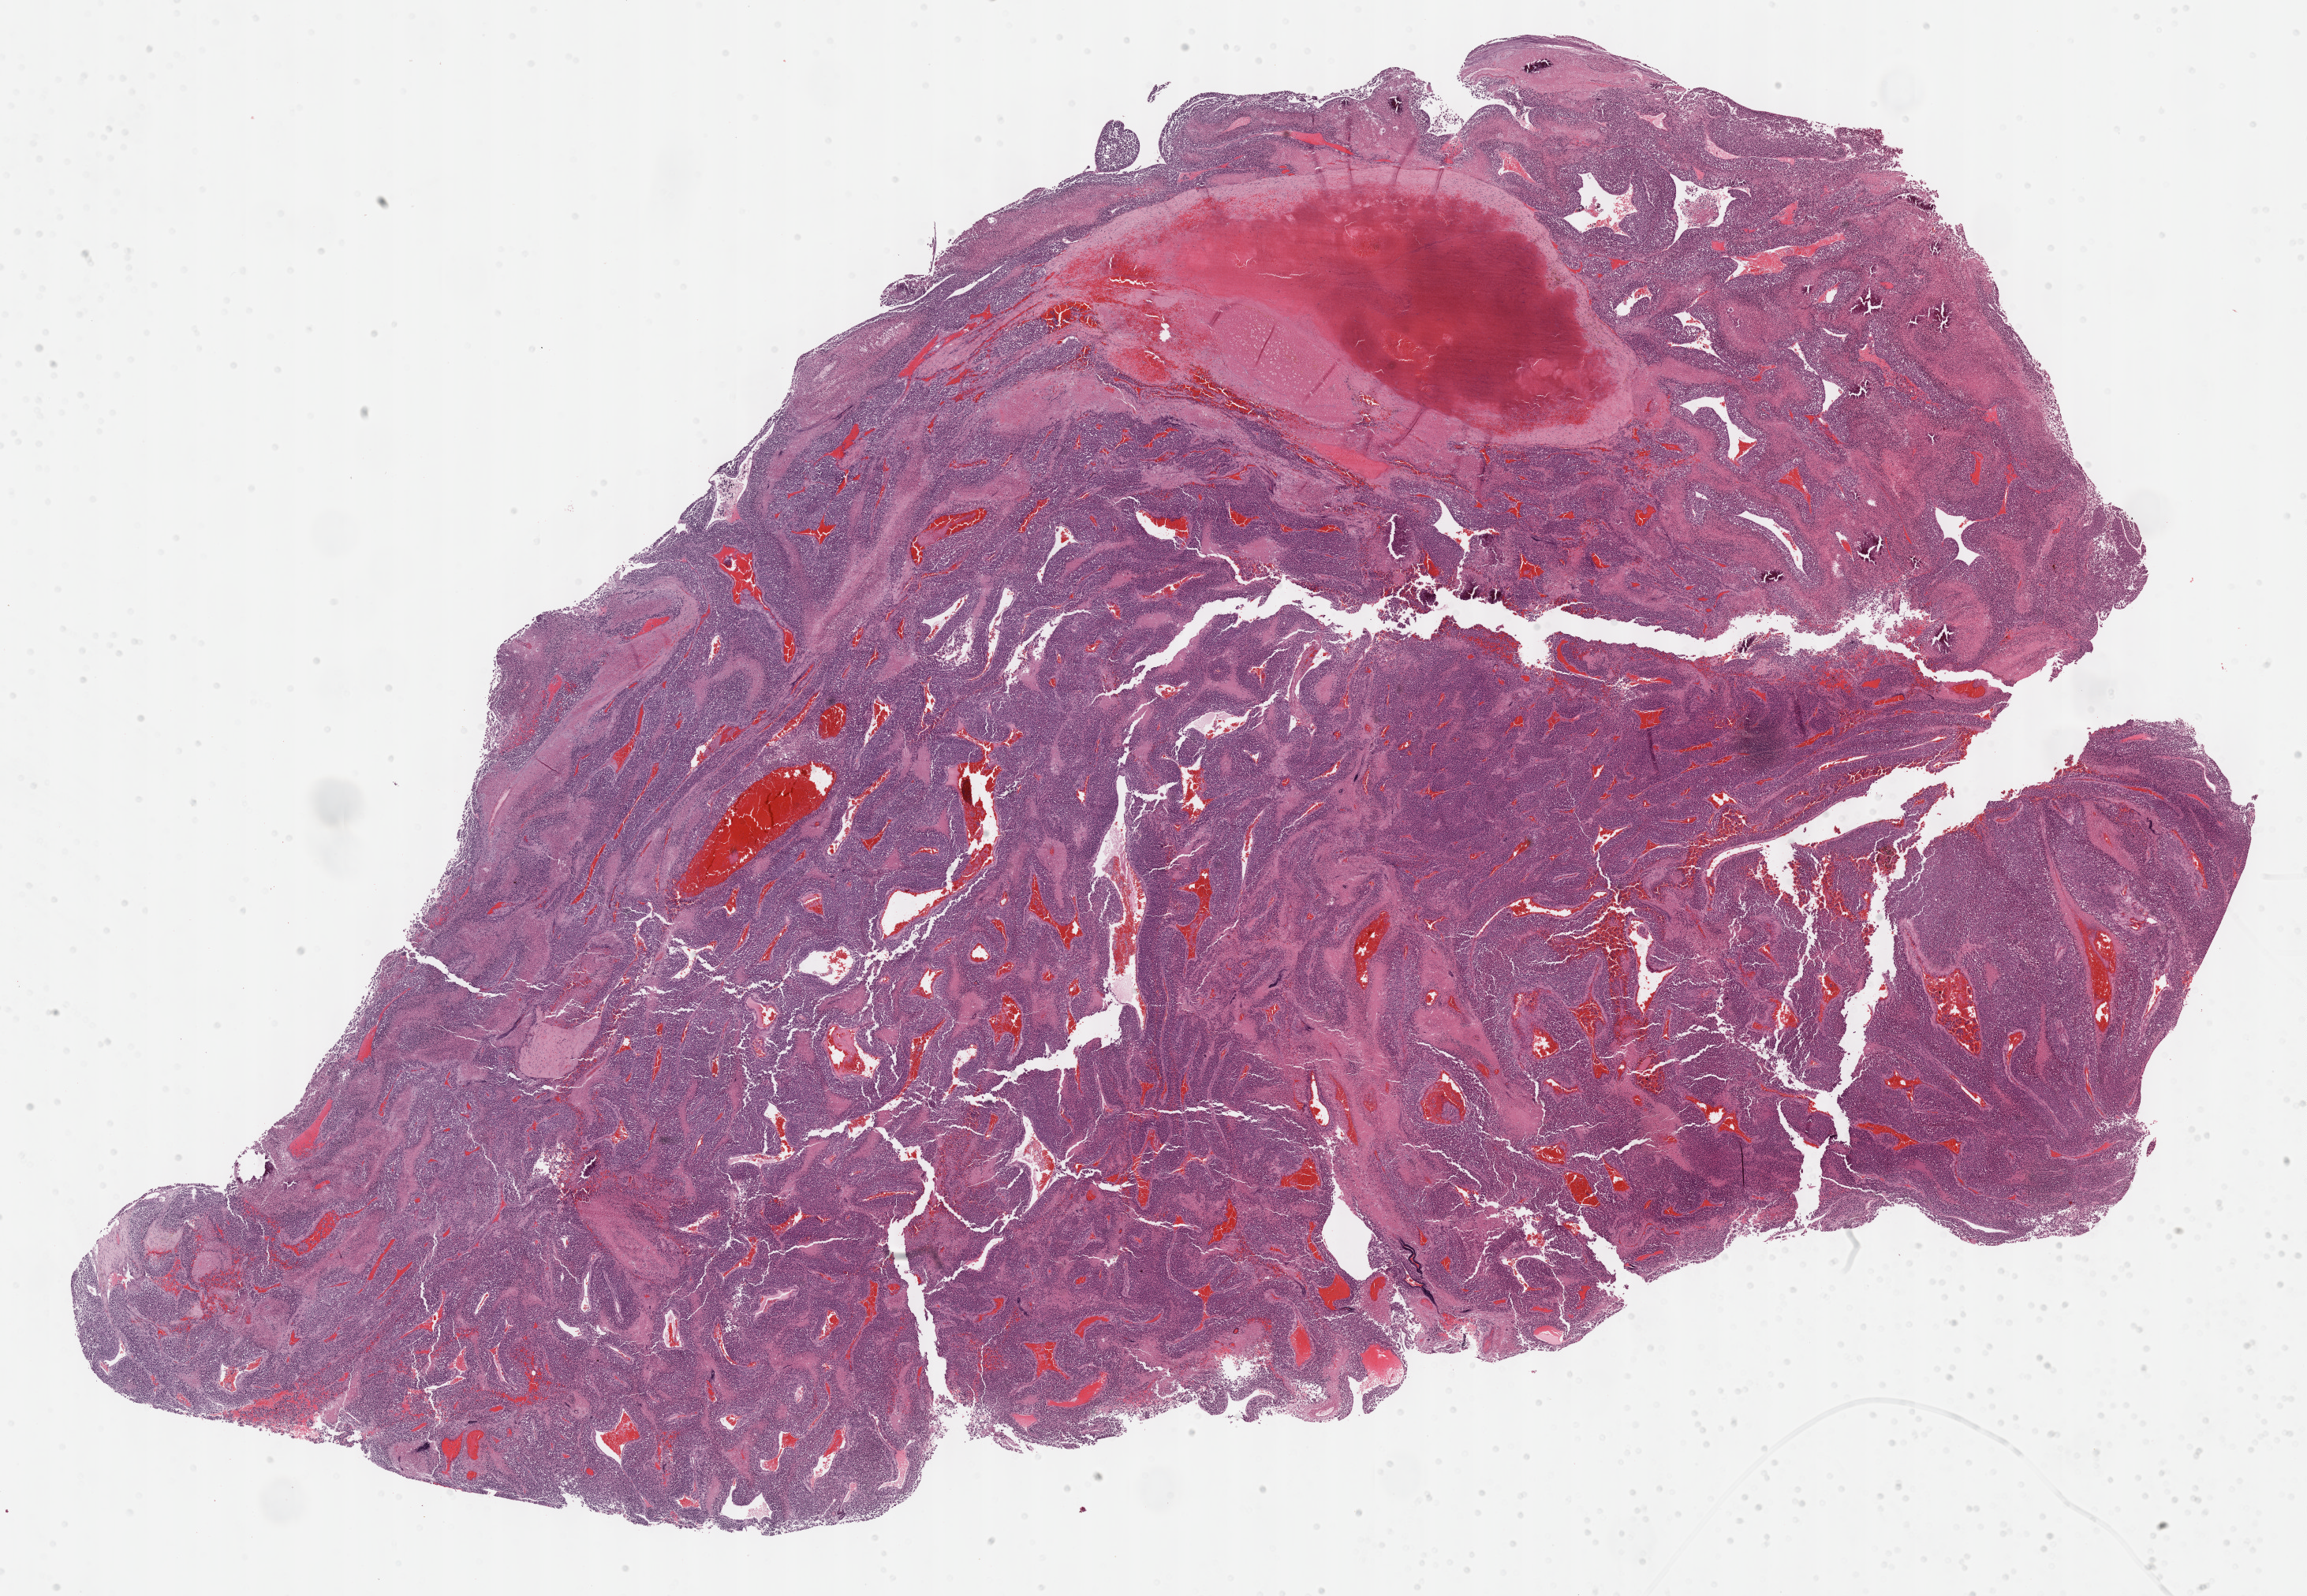
Whole-slide histology image, H&E-stained — shown as a low-resolution overview of the whole scanned area (about 23.7 x 16.4 mm, slide scanned at 40x). Formalin-fixed paraffin-embedded (FFPE) diagnostic section. Primary tumour sample from the adrenal cortex. Female, age 32 years at initial diagnosis.
Diagnosis: Adrenal cortical carcinoma. Laterality: right.